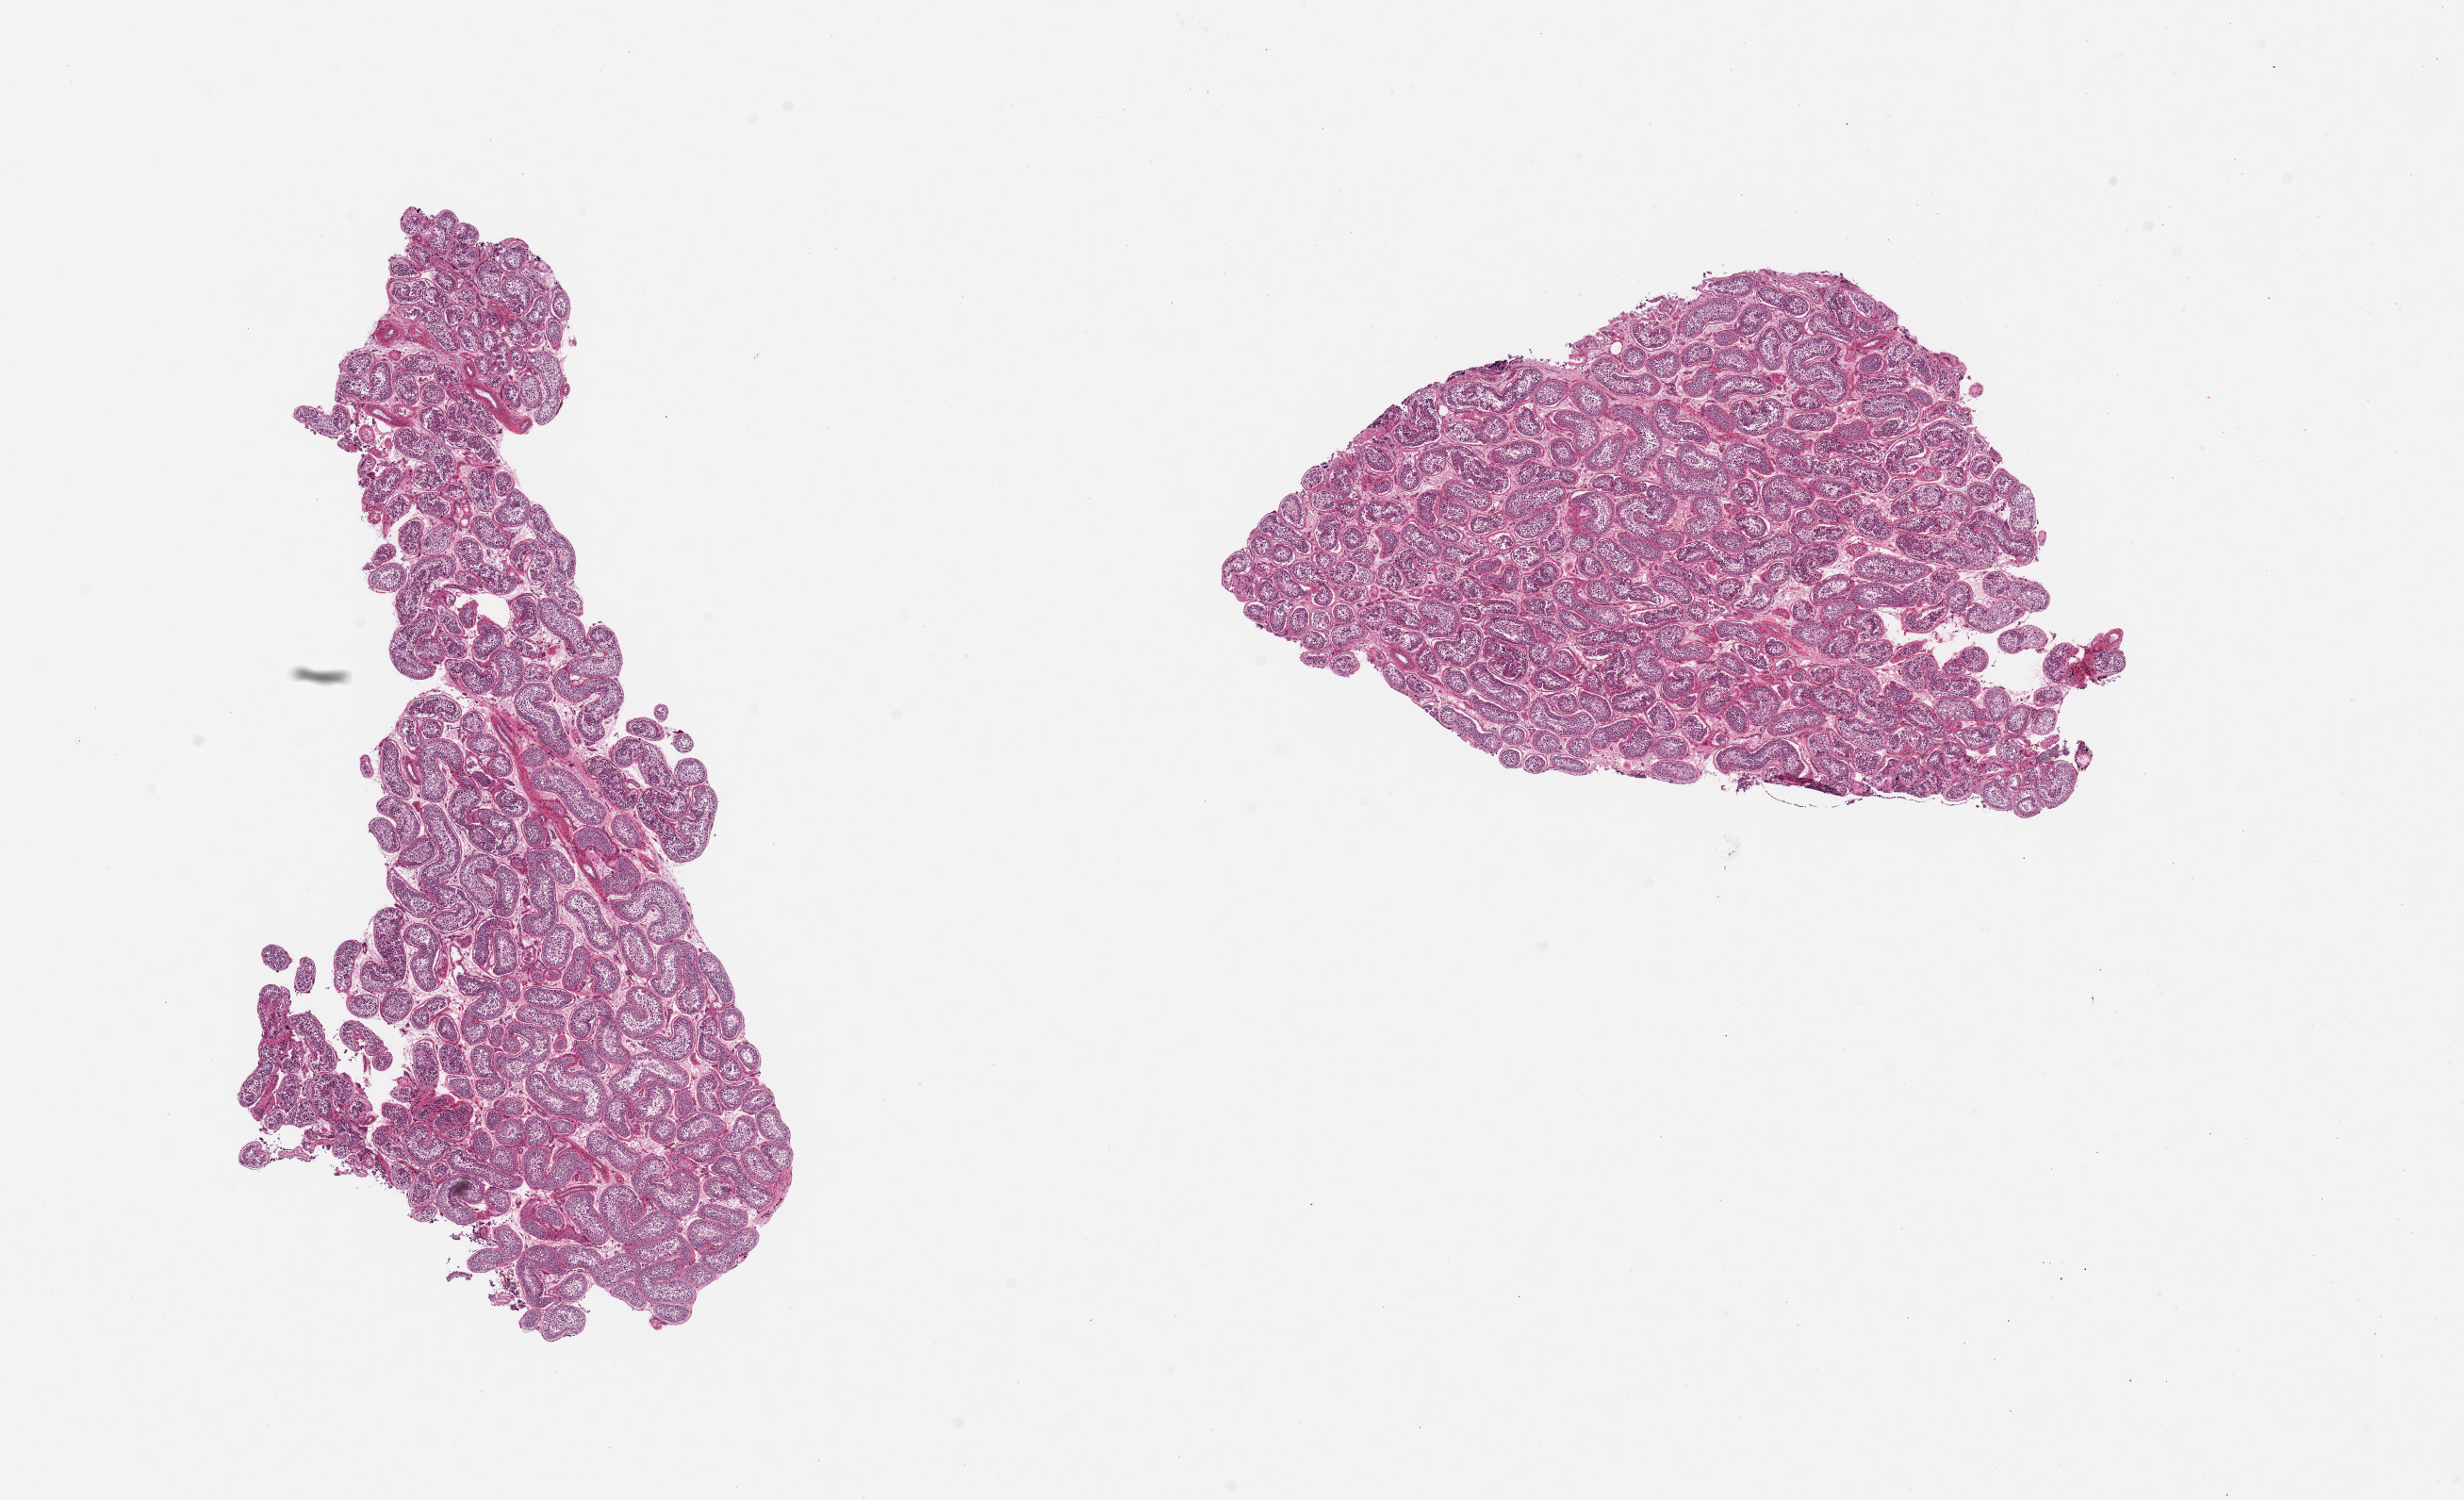
Digitized hematoxylin and eosin (H&E)-stained section — low-resolution overview of the scanned area, about 20.7 x 12.6 mm (from a 20x scan), PAXgene-fixed paraffin-embedded (PFPE) section, sampled site (target tissue): testis, tissue donor sample. Donor: male.
Review note (as recorded): 2 pieces, spermatogenesis present, appears reduced.